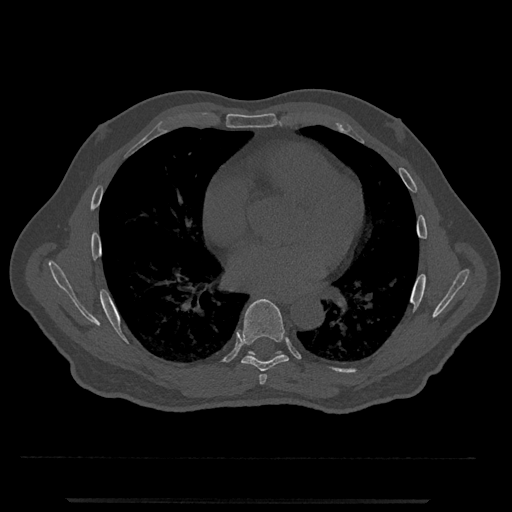
CT including the spine, one axial slice; 120 kVp; bone window (W 1800 / L 400 HU); 0.5 mm slice thickness; 512 × 512 image matrix, field of view 419 × 419 mm. Male patient, age 63 years. Case-level facts recorded for this patient, not image findings: primary cancer: prostate.
Outlined on this slice (semi-automatic segmentation, software-assisted and operator-edited):
- T6 vertebra: bounding box <259,374,267,385> (left, top, right, bottom; pixels)
- T7 vertebra: <236,299,289,372>
- T8 vertebra: <248,351,282,355>